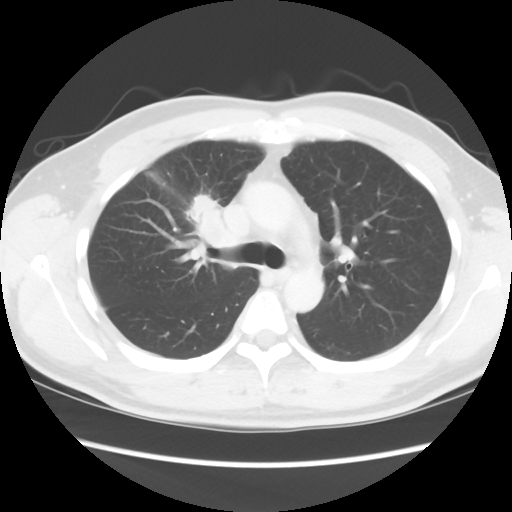
Chest CT, one axial slice. Position 61 of 80 along the scan axis. 120 kVp. Lung window (W 1500 / L -600 HU). 512 × 512 image matrix, field of view 360 × 360 mm. Patient: male, 35 years. Case-level facts recorded for this patient, not image findings: clinical TNM (as recorded): T1c N1 M1b.
Outlined on this slice (rectangle marked by the reading radiologist):
- lung tumour (recorded histology: adenocarcinoma): bounding box [x1, y1, x2, y2] px = [184, 192, 242, 253]